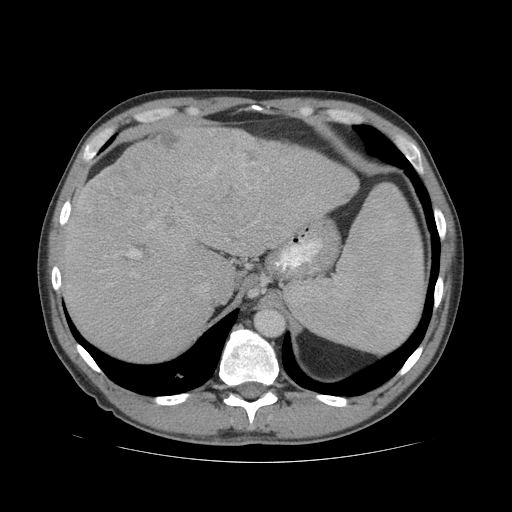
Contrast-enhanced abdominal CT (liver protocol), one axial slice; position 53 of 81 along the scan axis; 140 kVp; soft-tissue window (W 400 / L 40 HU); 2.5 mm slice thickness; 512 × 512 image matrix, field of view 400 × 400 mm. Case-level facts recorded for this patient, not image findings: diagnosis: hepatocellular carcinoma (patient treated with transarterial chemoembolisation; whether this scan precedes or follows treatment is not stated here); TNM stage (as recorded): Stage-IVB; Child-Pugh class: B; tumour differentiation: well differentiated; tumour nodularity: multinodular.
Structures marked on this image (semi-automatic segmentation, software-assisted and operator-edited):
- liver parenchyma outside the tumour (the mass and vessels are separate outlines, so this box may not span the whole liver): bounding box (x1, y1, x2, y2) in pixels: (62, 126, 358, 360)
- mass: (76, 124, 263, 229)
- liver vessels: (99, 167, 269, 292)